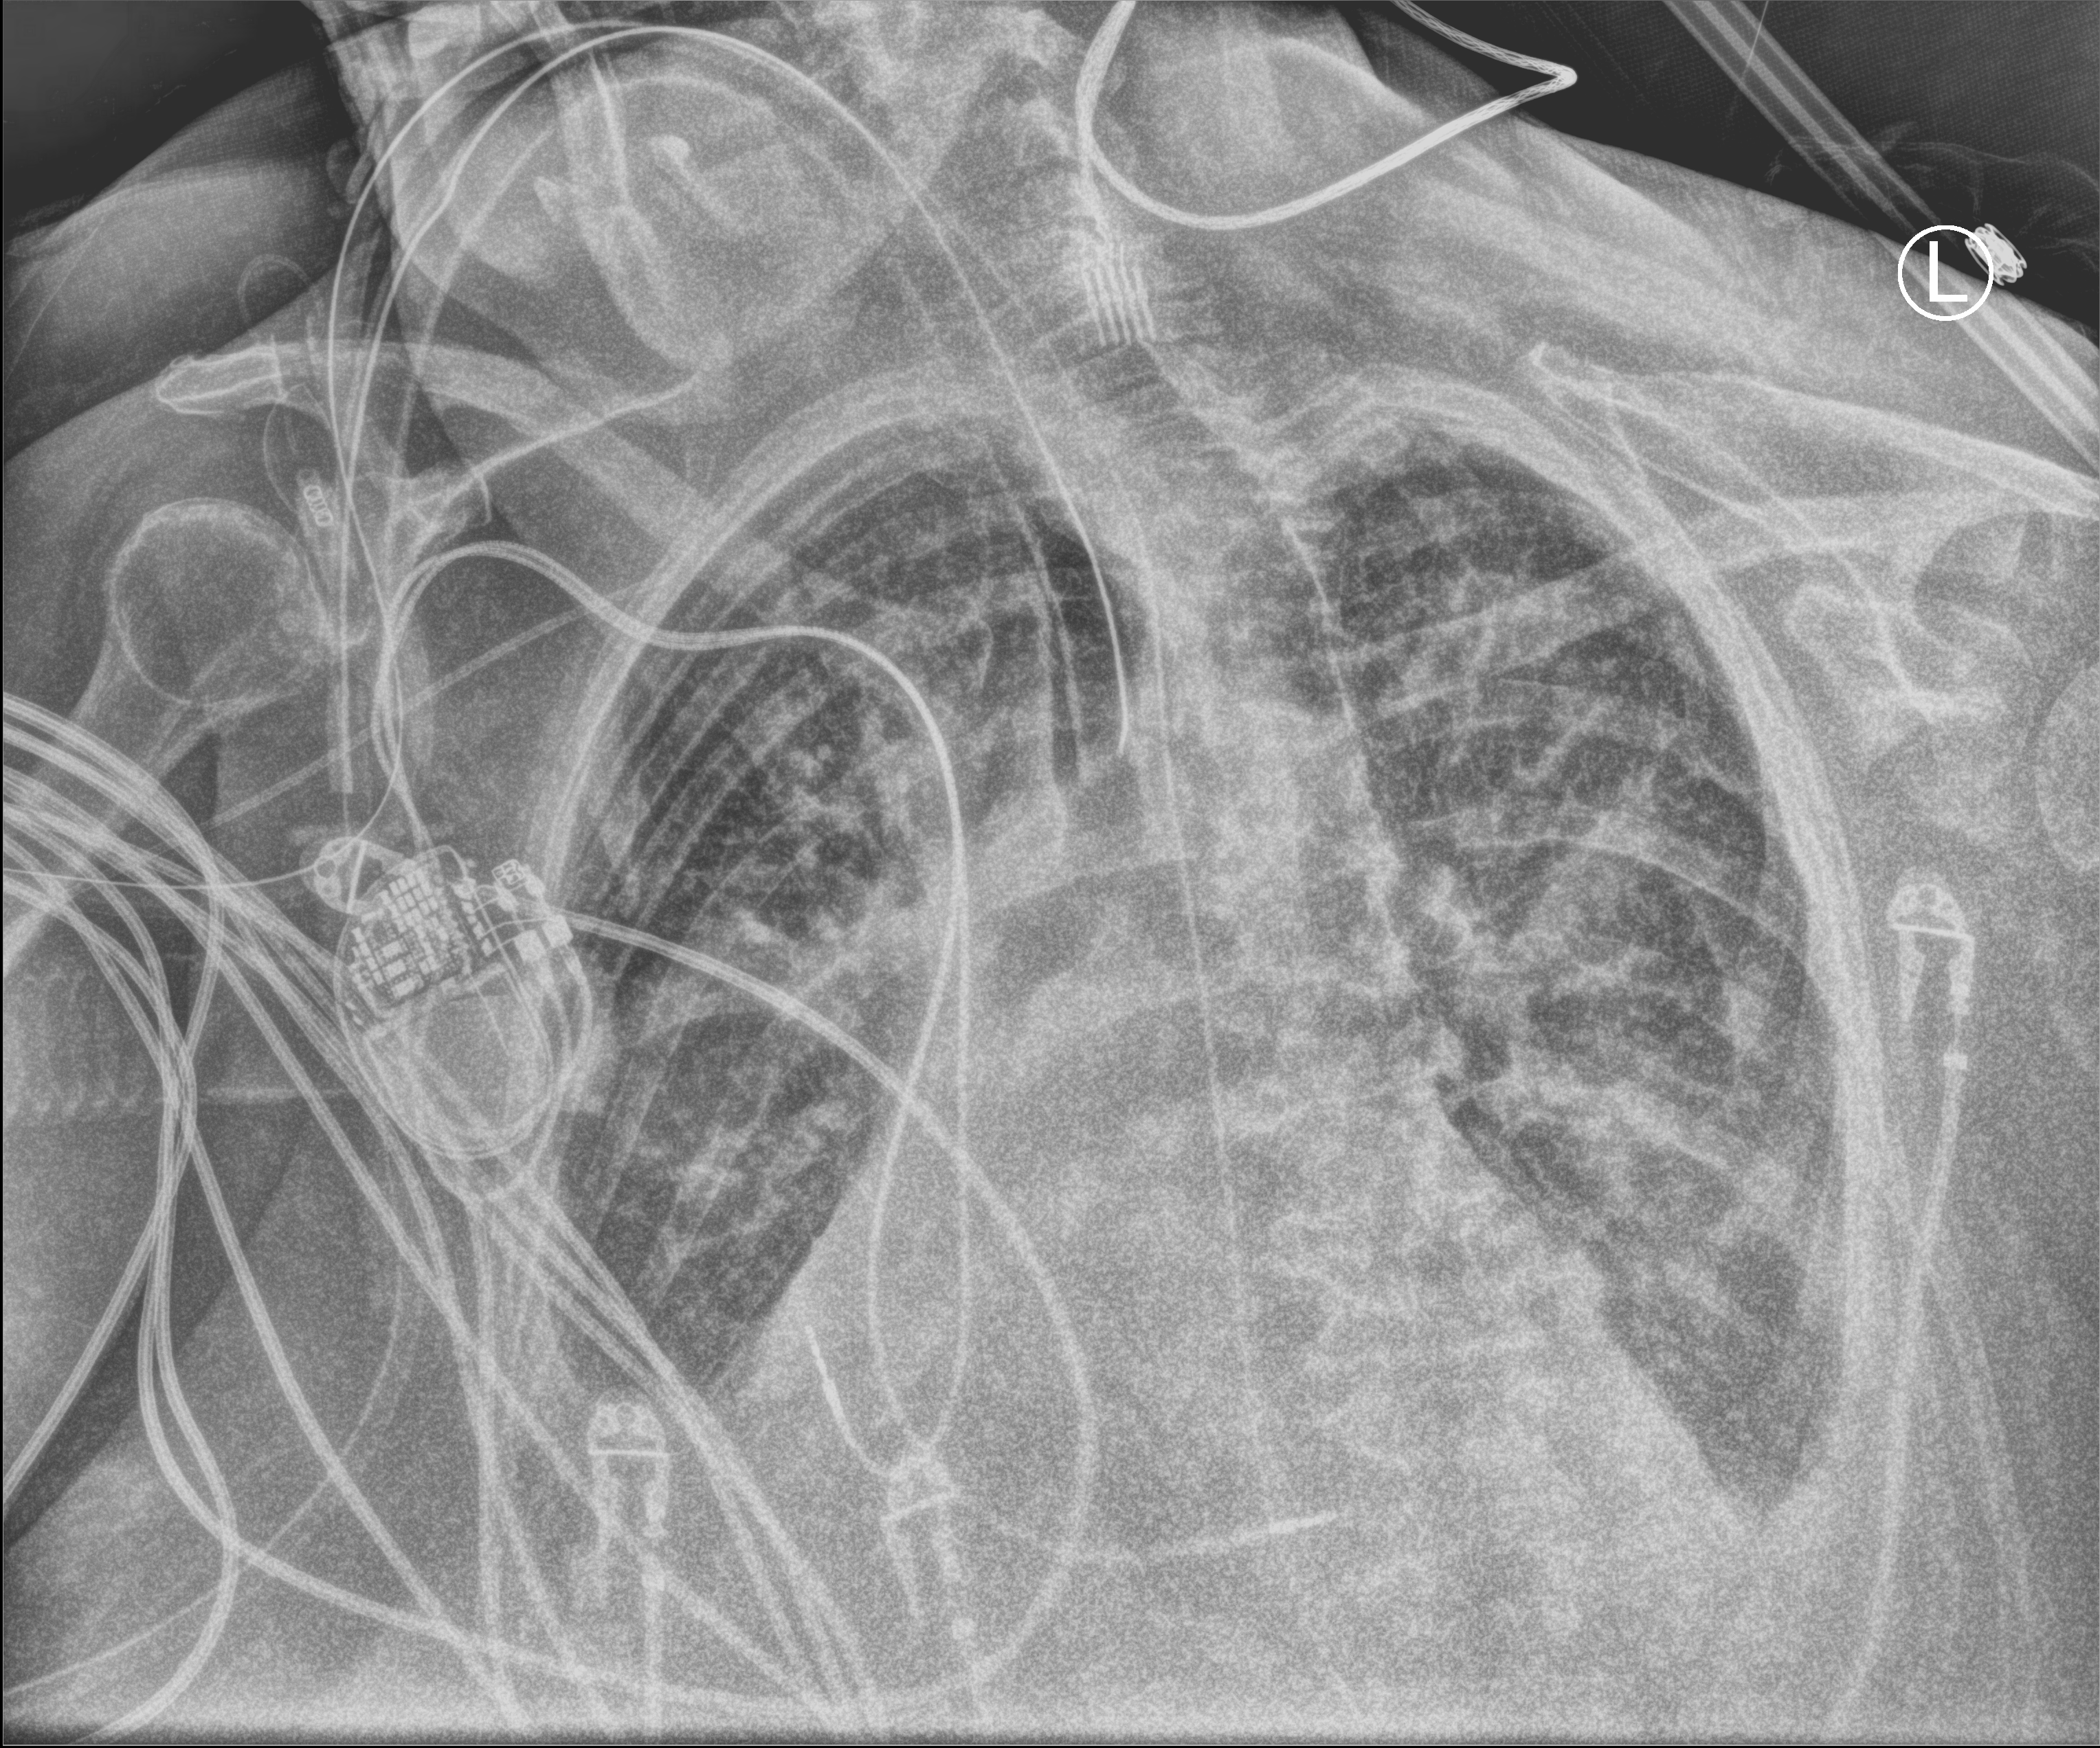
Chest X-ray (portable), anteroposterior (AP) projection. Female patient hospitalised with COVID-19, age 75–90 years.
From the hospital-stay record, not from the radiograph (when in the stay this image was taken is not recorded):
- admitted to intensive care during this hospital stay: yes